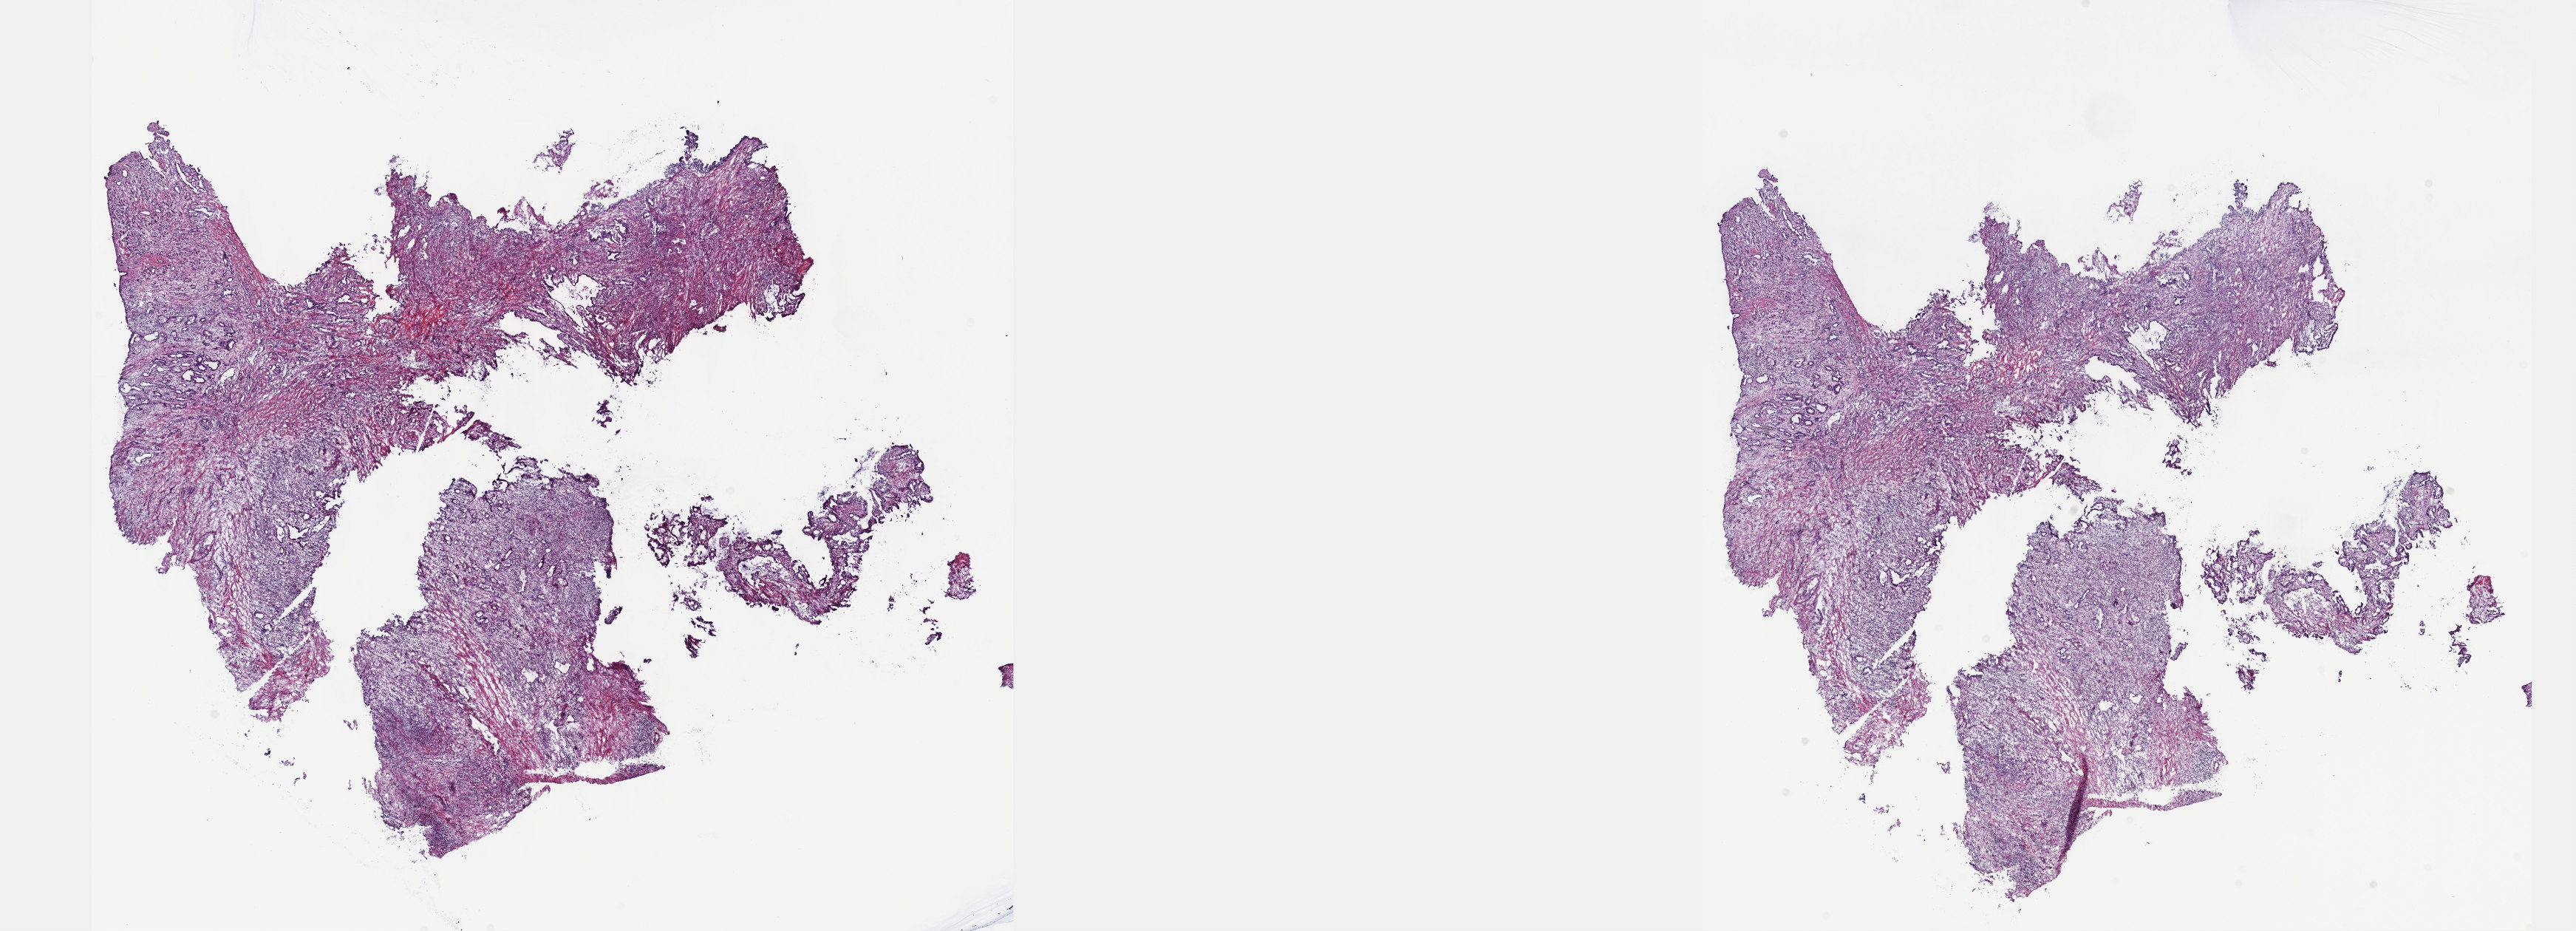
Whole-slide histology image, H&E, whole scanned area (about 28.2 x 10.2 mm, acquisition: 40x scan) shown as a low-resolution overview, frozen section from the top of the tissue portion, sample: primary tumour, pancreas. Patient: female, age at initial diagnosis 84 years. Histologic grade: G2 (moderately differentiated). Composition of this section per pathologist review: tumour cells 100%, tumour nuclei 60%, normal cells 0%, stromal cells 0%, necrosis 0%. Infiltration values recorded for this section: lymphocyte infiltration 8%, monocyte infiltration 1%, neutrophil infiltration 0%.
Lymph nodes positive (case pathology): 2 of 14 examined. AJCC pathologic stage: IIB (7th edition). Histologic diagnosis: Infiltrating duct carcinoma, NOS. TNM: T3 N1 M0.